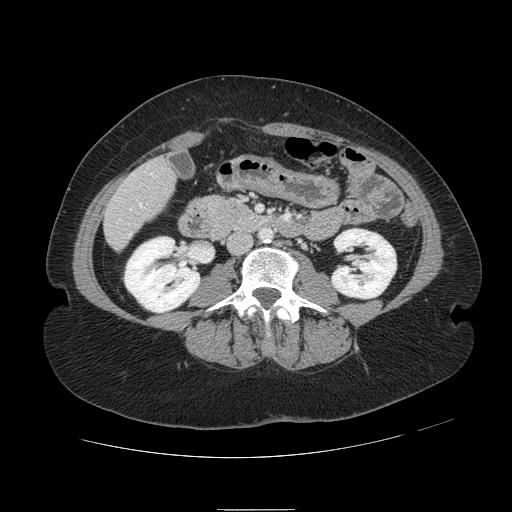
Contrast-enhanced abdominal CT, one axial slice. Slice 18 of 121 in the series (ordered by position). 120 kVp. Soft-tissue window (W 400 / L 40 HU). 2.5 mm slice thickness. 512 × 512 image matrix, field of view 400 × 400 mm. Female patient, age 52 years. Case-level facts recorded for this patient, not image findings: diagnosis: colorectal cancer liver metastases, imaged before liver resection; multiple liver metastases: yes; largest metastasis: 6.3 cm.
Outlined on this slice (outlined manually by an expert reader):
- hepatic veins: box from (x=140, y=174) to (x=153, y=207) px
- liver: (x=105, y=162)–(x=173, y=247)